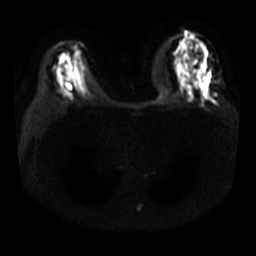
Breast MRI, one axial slice; diffusion-weighted series; image 2 of 4 stored at this slice position (different b-values; order by instance number); 3 T; 5 mm slice thickness; 256 × 256 image matrix, field of view 340 × 340 mm. Female patient.
Outlined on this slice (outlined manually by an expert reader):
- tumour on diffusion-weighted imaging: bounding box <201,64,208,82> (left, top, right, bottom; pixels)